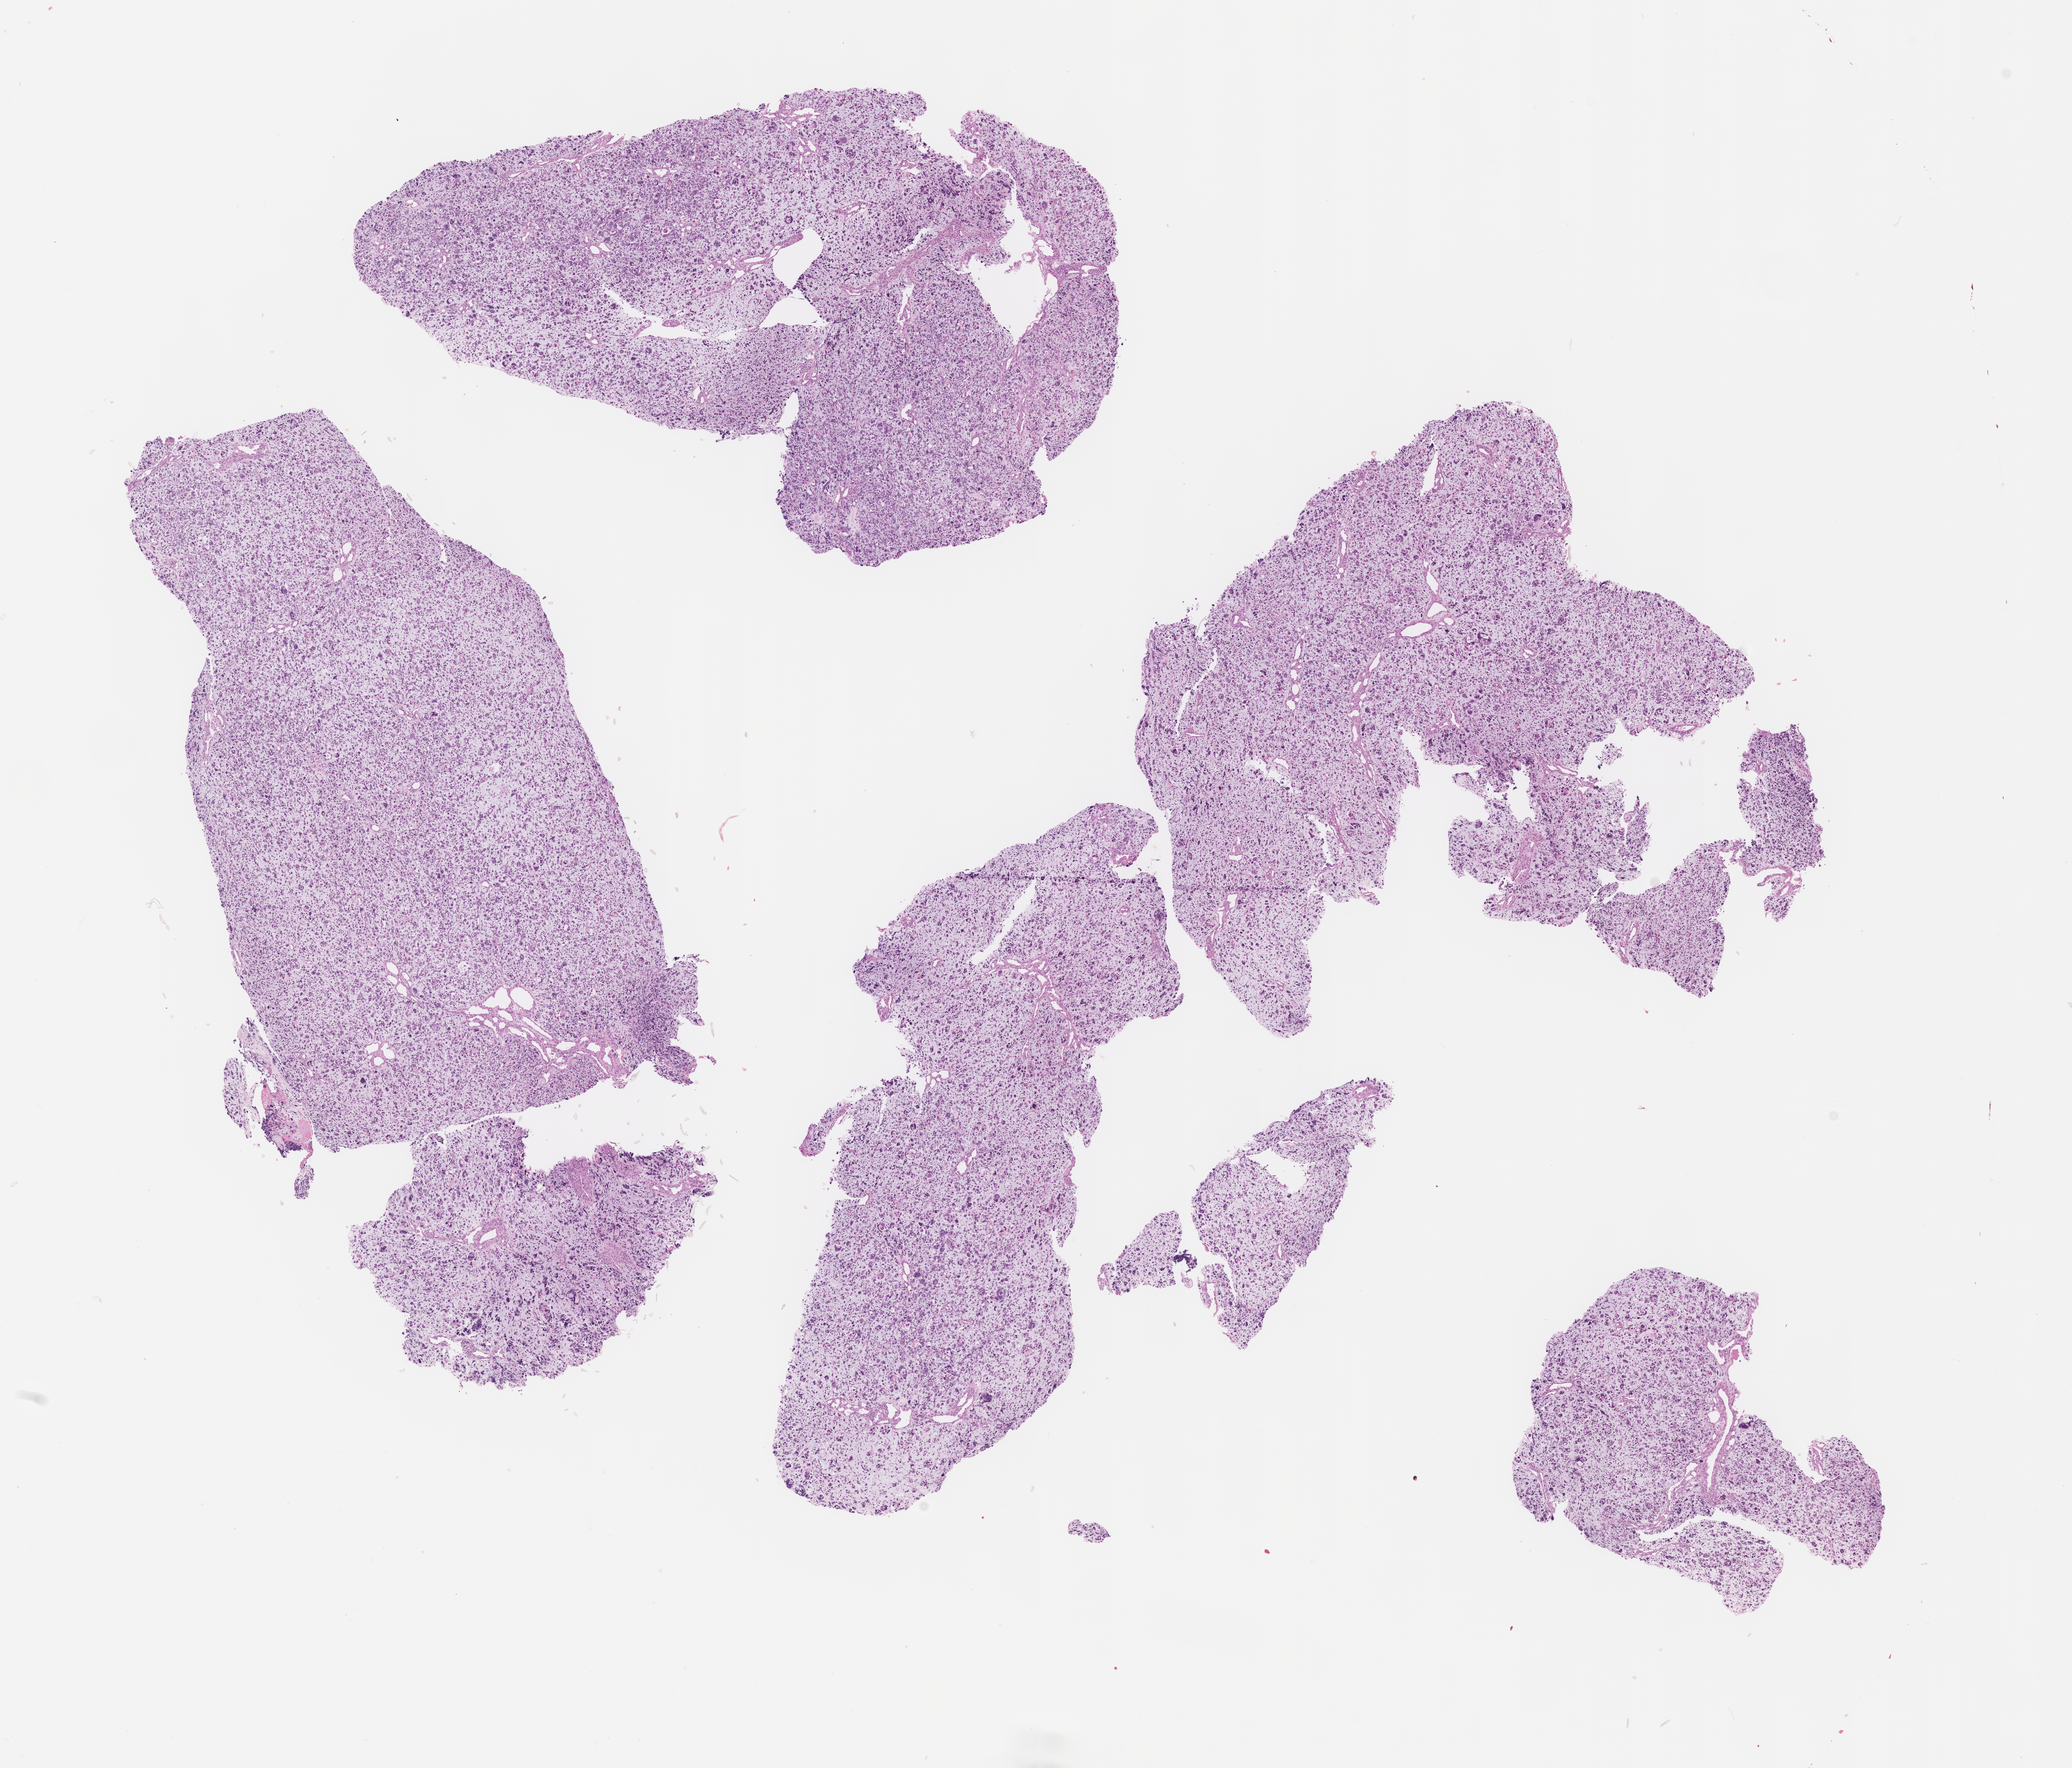
Whole-slide image, H&E stain of tumor tissue, whole scanned area (about 14.1 x 12.0 mm) shown as a low-resolution overview; formalin-fixed paraffin-embedded section; site: eyelid, left. Patient: male, age 7.7 years at diagnosis.
Stage (as recorded): 1. Diagnosis: rhabdomyosarcoma; histological classification: embryonal rhabdomyosarcoma. Metastatic status at presentation (as recorded): non-metastatic (confirmed).